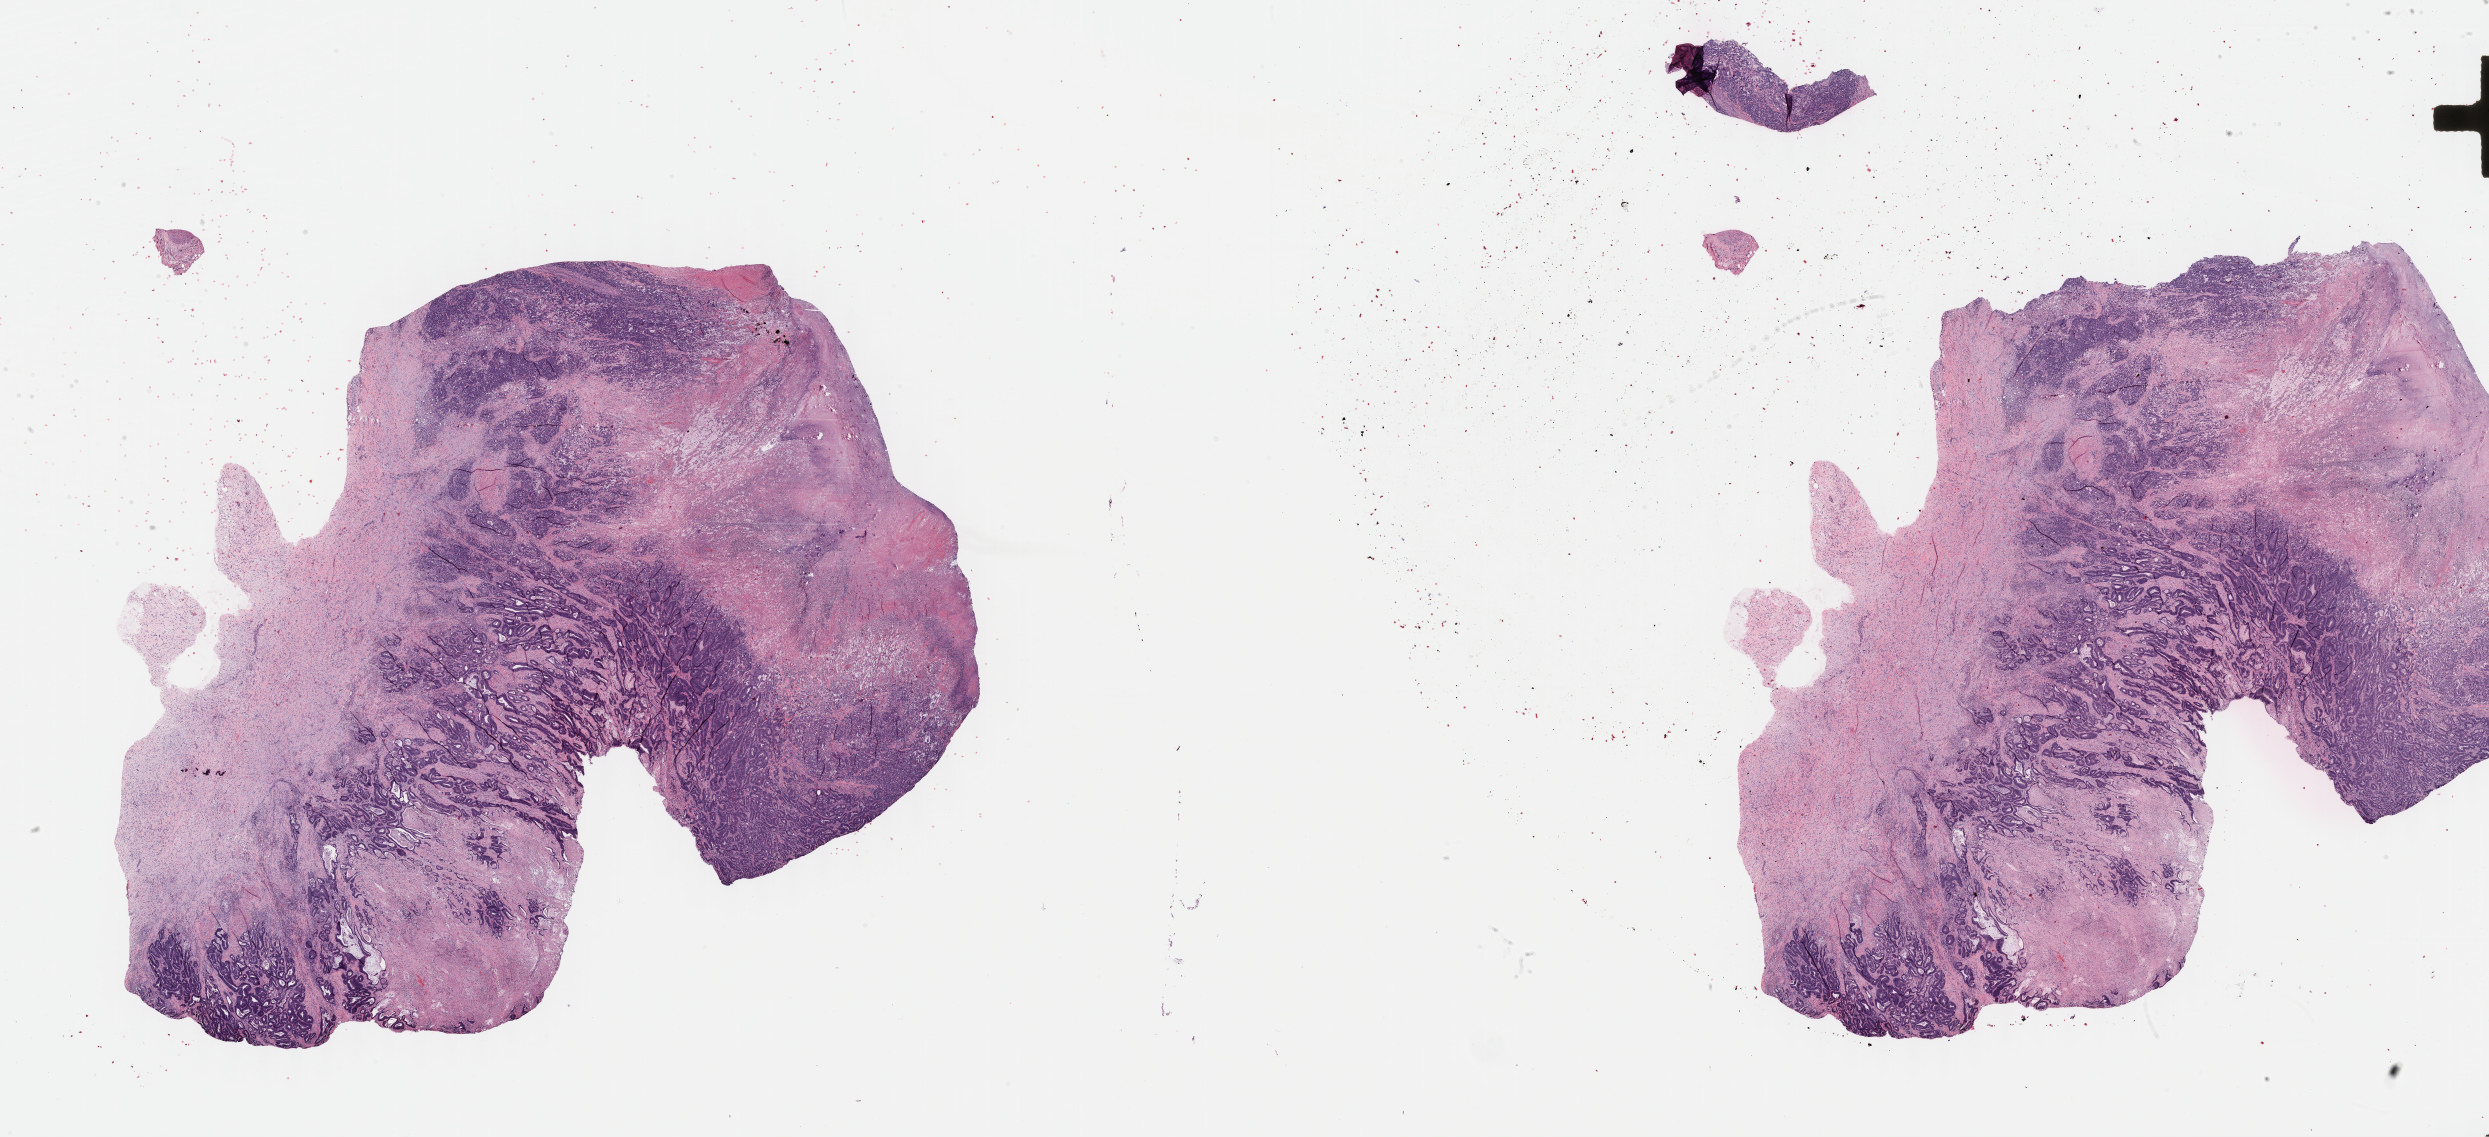
Digitized Hematoxylin and eosin (H&E) stained tissue section (whole slide) — a low-resolution overview of the entire scanned area, about 40.3 x 18.4 mm (slide scanned at 40x); FFPE section; colon, primary tumour sample. Patient: female, age at initial diagnosis 55 years.
Diagnosis: Adenocarcinoma, NOS (cecum). Lymph nodes positive (case pathology): 11 of 15 examined. AJCC pathologic stage: IIIC (7th edition).